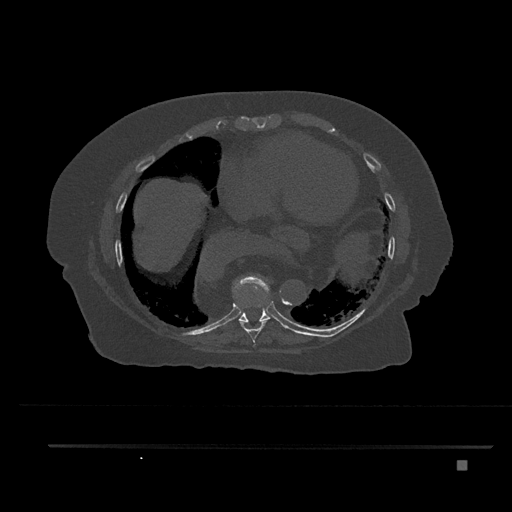
CT including the spine, one axial slice; slice 421 of 797 in the series (ordered by position); bone window (W 1800 / L 400 HU); 512 × 512 image matrix. Female patient, age 76 years. Case-level facts recorded for this patient, not image findings: primary cancer: lung; vertebrae with lytic lesions (as recorded): T11, L3.
Structures marked on this image (semi-automatic segmentation, software-assisted and operator-edited):
- T8 vertebra: box from (x=238, y=289) to (x=270, y=347) px
- T9 vertebra: (x=226, y=275)–(x=272, y=324)